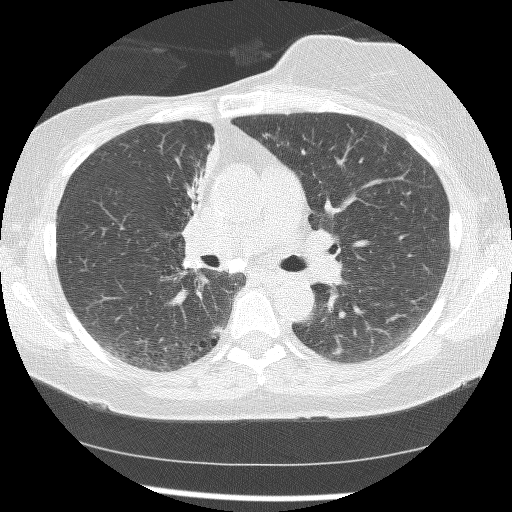
Low-dose screening chest CT, axial slice. Baseline screening round. Lung window (W 1500 / L -600 HU). Slice 65 of 172 in the series. Female, age 56 years at enrolment. Current smoker at enrolment.
Lesion marked by an expert reader, box from (x=161, y=137) to (x=215, y=255) px. The screening reader recorded 2 non-calcified nodules or masses ≥4 mm on this exam (right lower lobe, right middle lobe); which of them this box marks is not recorded.